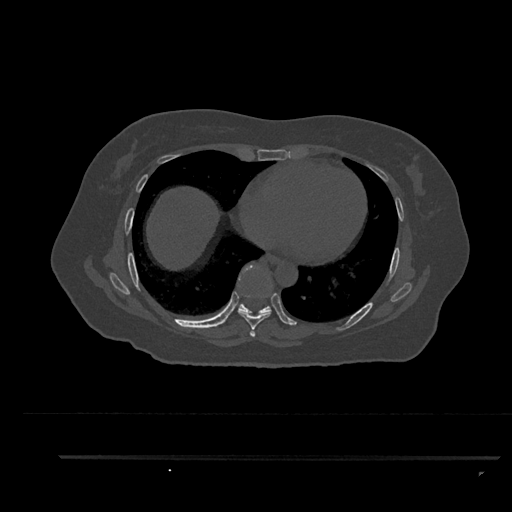
CT including the spine, one axial slice. Position 489 of 797 along the scan axis. Bone window (W 1800 / L 400 HU). 0.5 mm slice thickness. 512 × 512 image matrix, field of view 408 × 408 mm. Patient: female, 44 years. Case-level facts recorded for this patient, not image findings: primary cancer: renal; vertebrae with lytic lesions (as recorded): L1.
Structures marked on this image (semi-automatic segmentation, software-assisted and operator-edited):
- T6 vertebra: bounding box <251,334,255,336> (left, top, right, bottom; pixels)
- T7 vertebra: <238,310,271,337>
- T8 vertebra: <238,265,272,316>